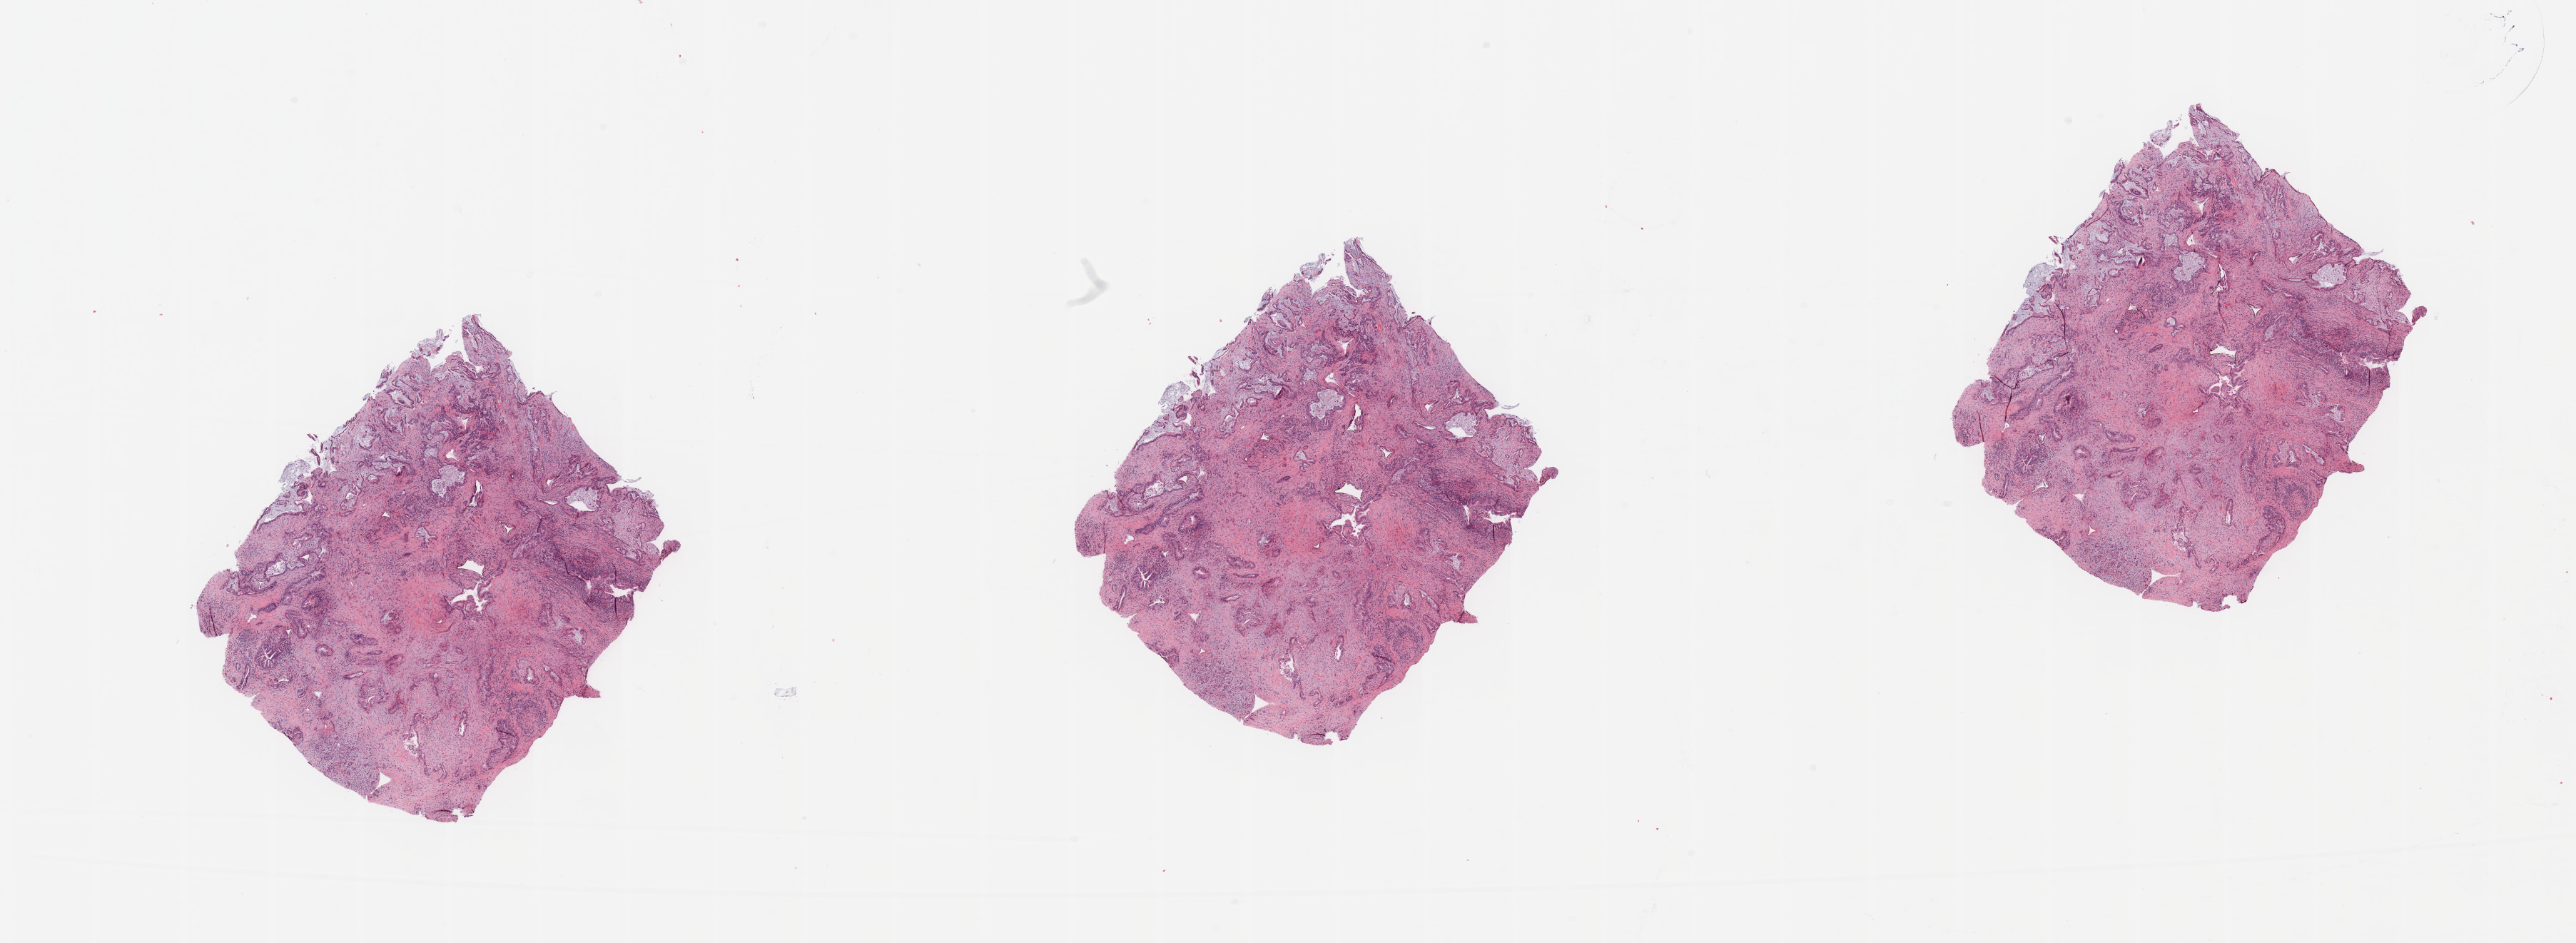
H&E-stained whole-slide image — a low-resolution overview of the entire scanned area, about 28.5 x 10.4 mm, tumour tissue sample, pancreas. Patient: female, age 67 years. Histologic grade: G2 (moderately differentiated).
AJCC pathologic stage: III. Histologic diagnosis: Infiltrating duct carcinoma, NOS.